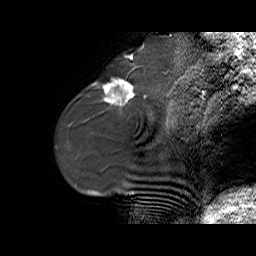
Breast MRI (dynamic contrast-enhanced), one sagittal slice. Slice 19 of 70 in the series (ordered by position). Dynamic contrast-enhanced series, time point 2 of 6 at this slice position (early post-contrast). 1.5 T. TE 5.5 ms, TR 32.9 ms. 4 mm slice thickness. 256 × 256 image matrix. Female patient. Case-level facts recorded for this patient, not image findings: setting: breast cancer imaged before/during neoadjuvant chemotherapy; receptor status: HER2-positive.
Structures marked on this image (semi-automatic segmentation, software-assisted and operator-edited):
- analysis volume of interest (the breast-tissue region the enhancement analysis was run in; not a lesion): bounding box <96,73,141,114> (left, top, right, bottom; pixels)
- tumour enhancement mask (voxels above the 100 % enhancement threshold inside the analysis volume of interest): <104,80,134,104>